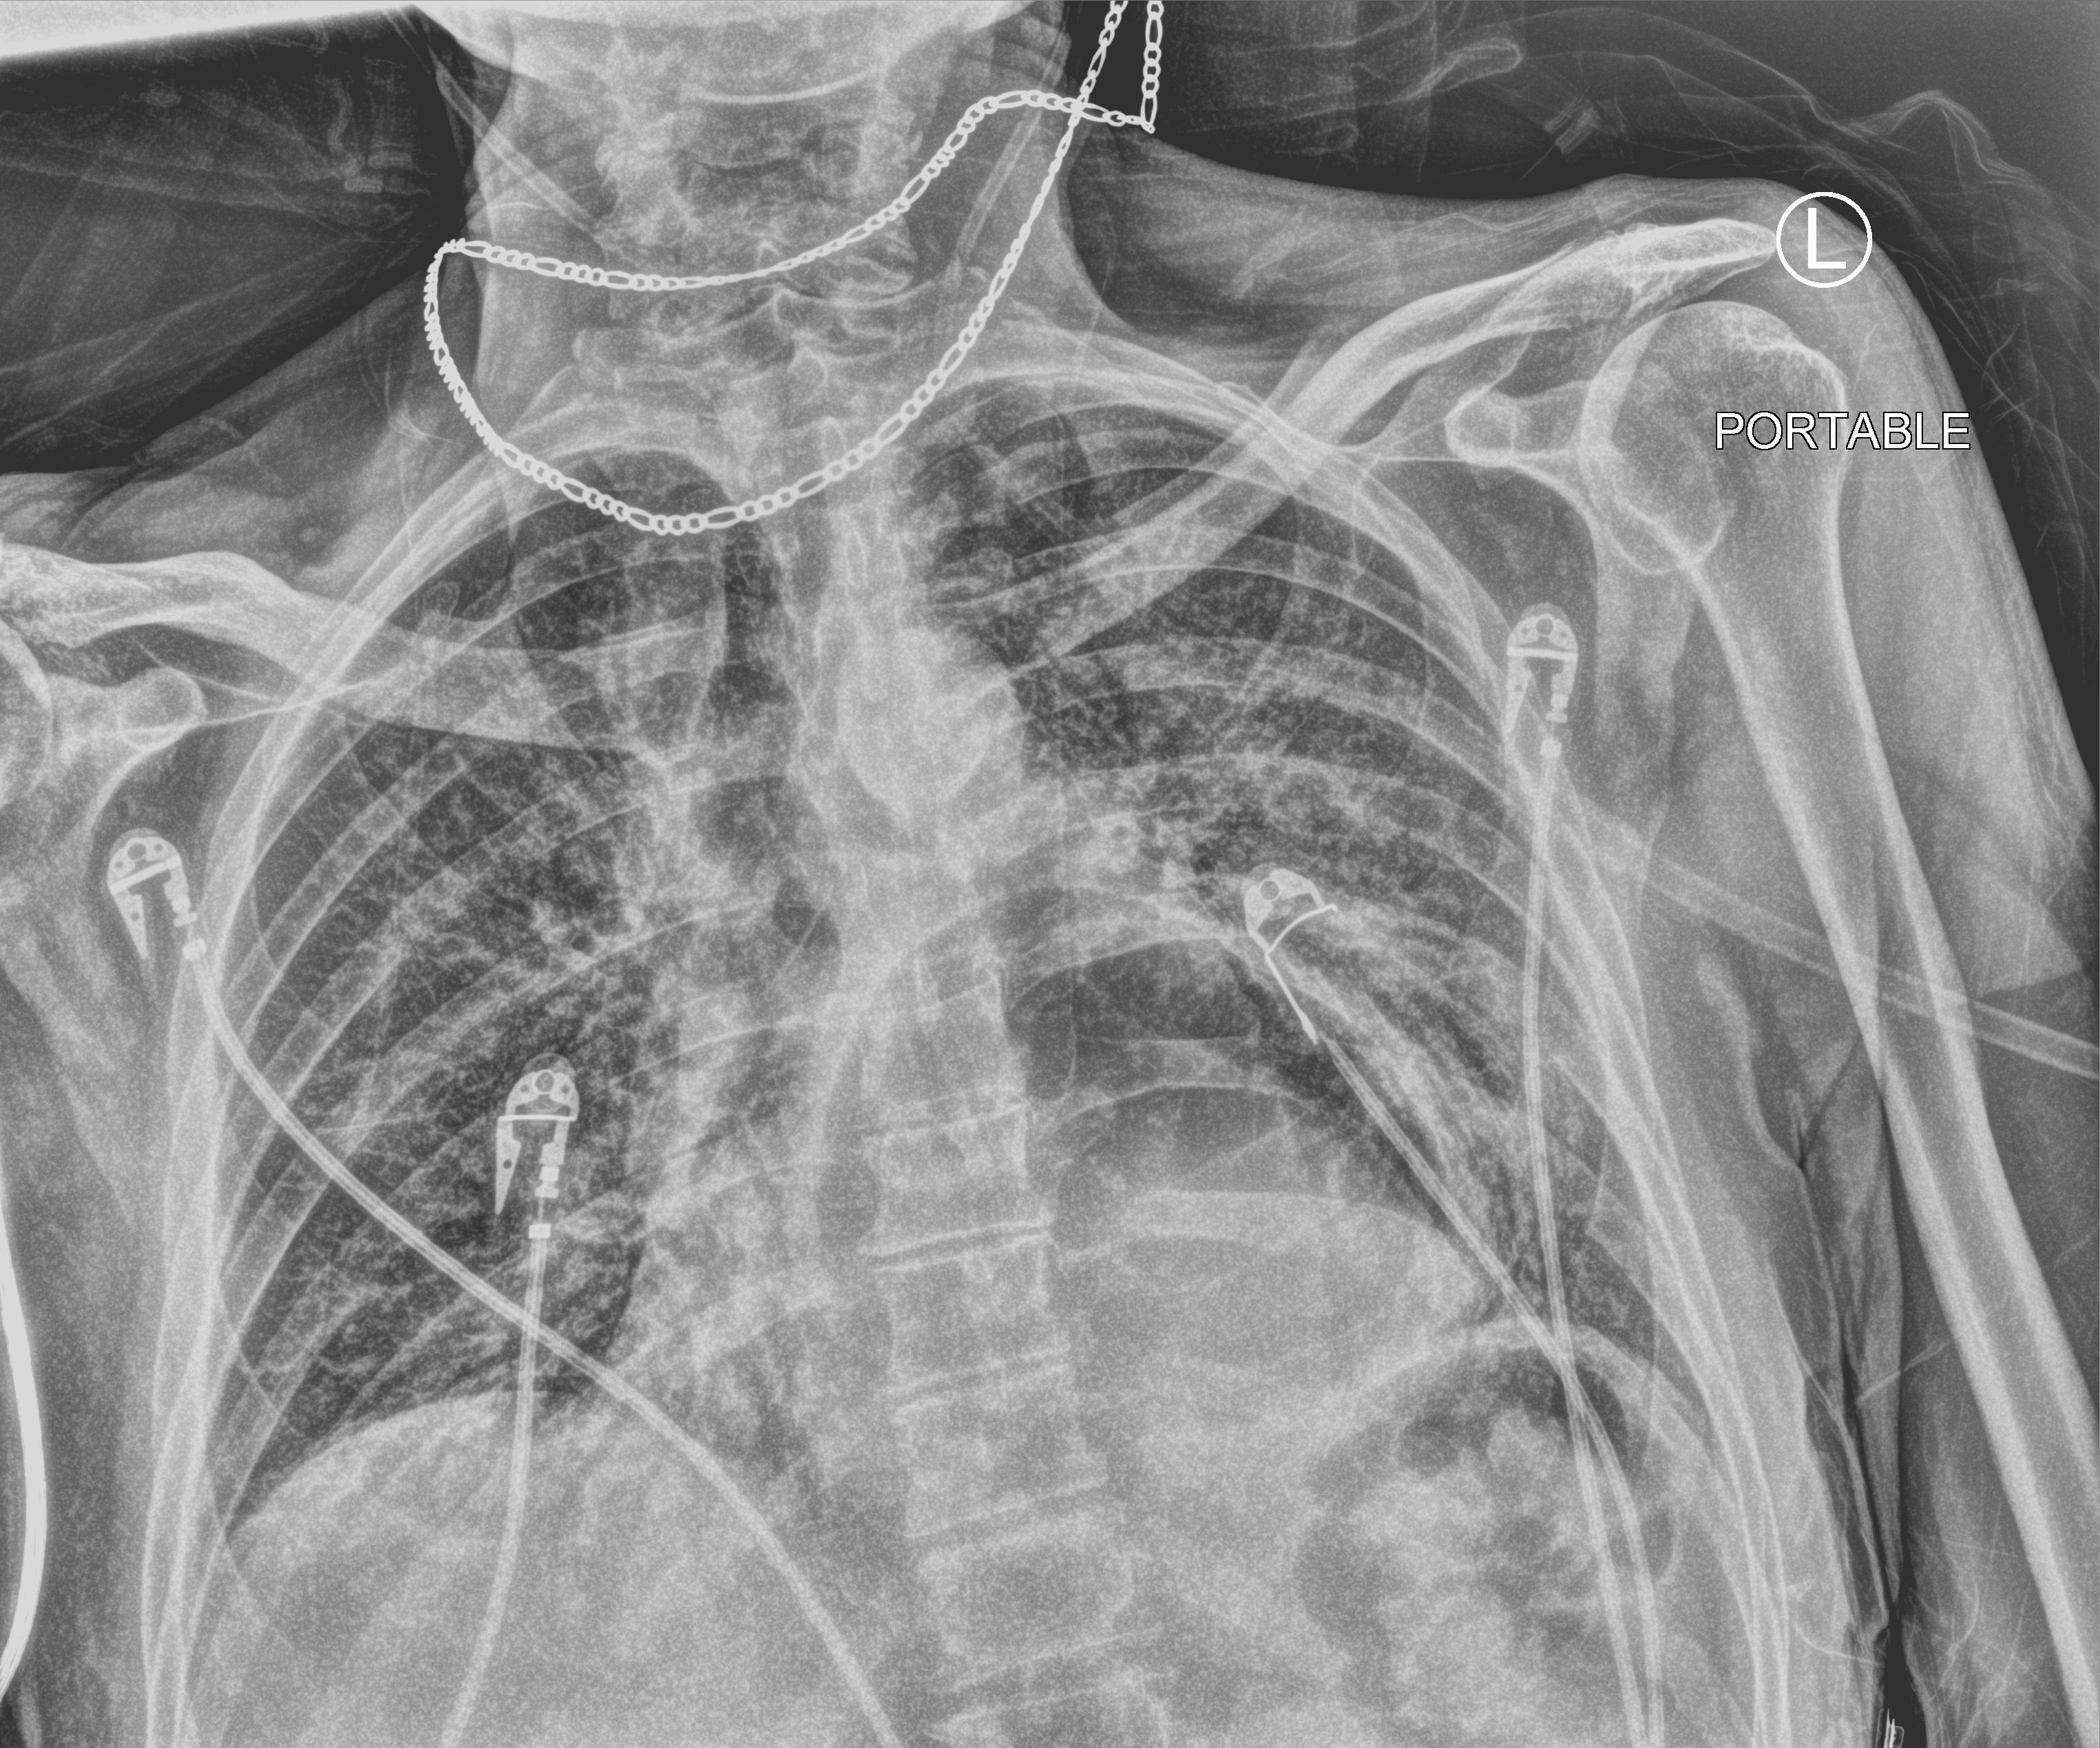
Chest X-ray (portable). Male patient hospitalised with COVID-19, age 75–90 years.
Admission-level facts for this patient (not findings on this image; timing relative to this image not recorded): mechanically ventilated during this hospital stay: yes; diabetes (admission record): yes.